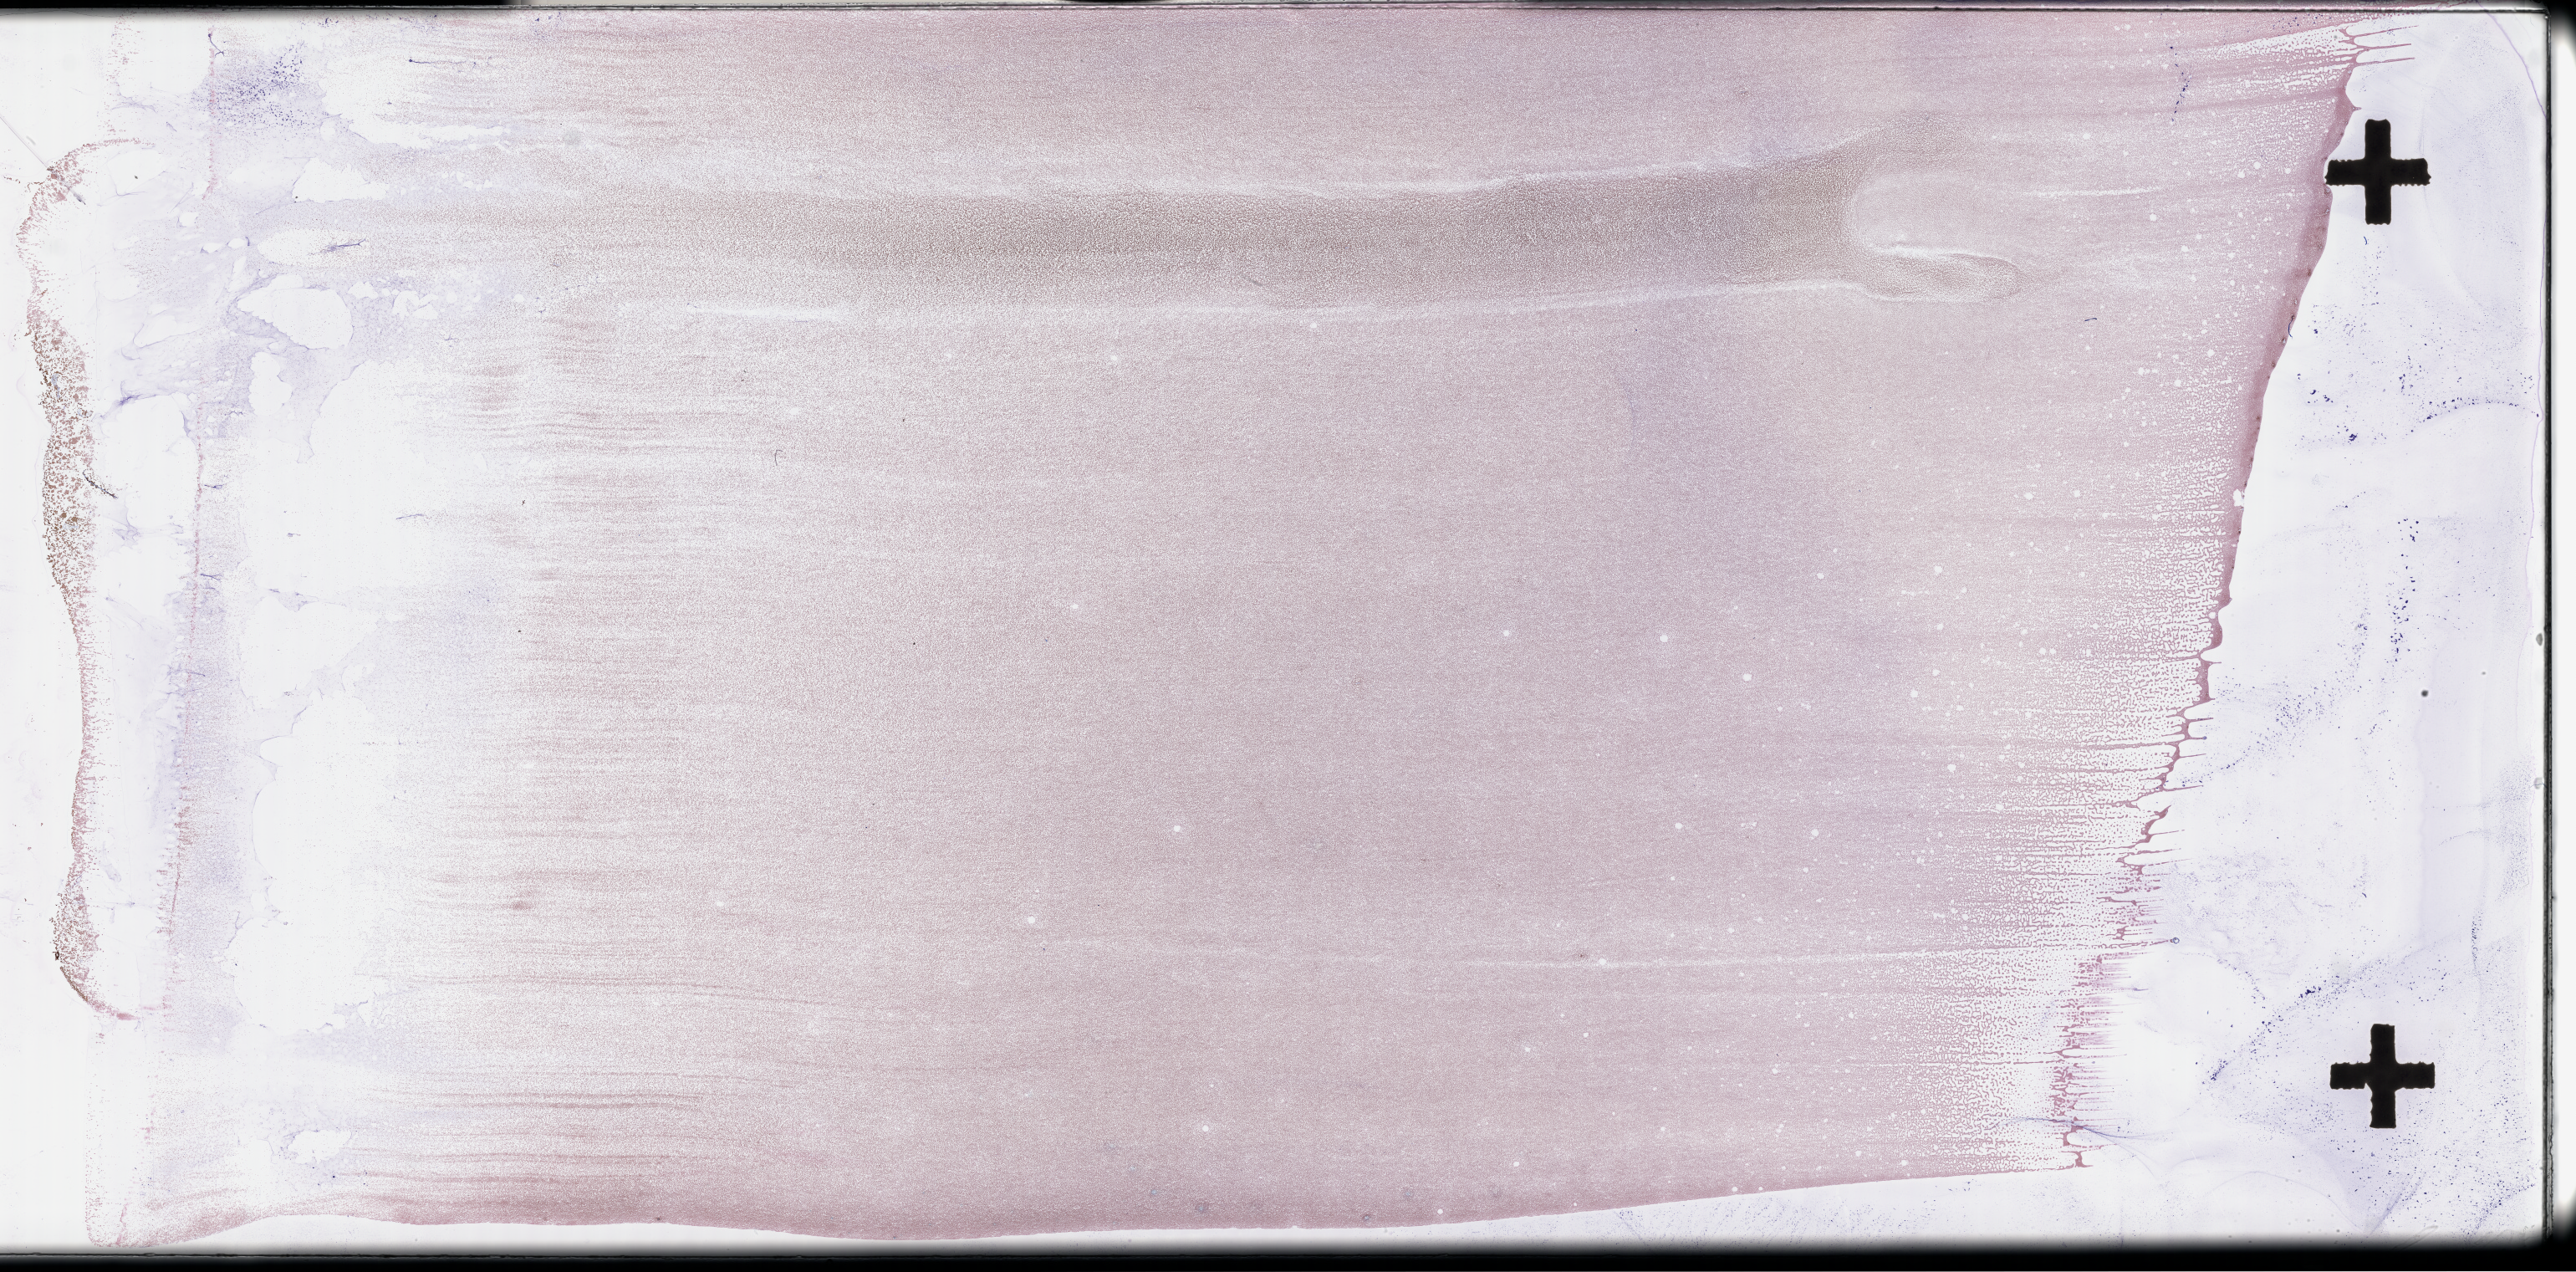
Wright-Giemsa-stained whole blood smear, whole-slide image, whole scanned area (about 49.8 x 24.6 mm) shown as a low-resolution overview, EDTA-anticoagulated smear. Female patient.
• from a patient with: Acute Myeloid Leukemia Not Otherwise Specified